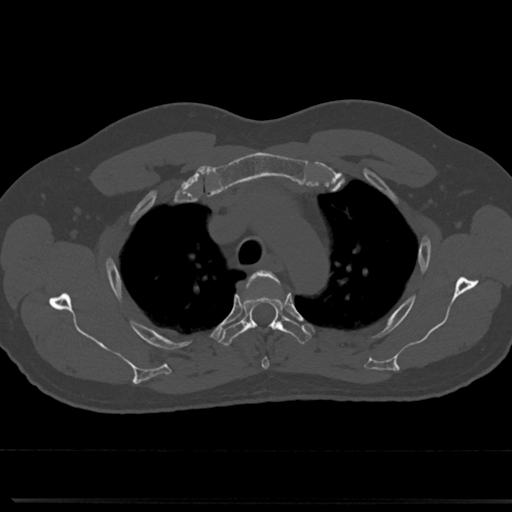
CT including the spine, one axial slice; position 562 of 817 along the scan axis; reconstruction kernel Br40s/3; bone window (W 1800 / L 400 HU); 0.5 mm slice thickness; 512 × 512 image matrix, field of view 355 × 355 mm. Male patient, age 61 years. From the clinical record (not read from this slice): primary cancer: prostate.
Outlined on this slice (semi-automatically segmented with operator editing):
- T3 vertebra: bounding box <252,271,290,368> (left, top, right, bottom; pixels)
- T4 vertebra: <219,274,311,346>